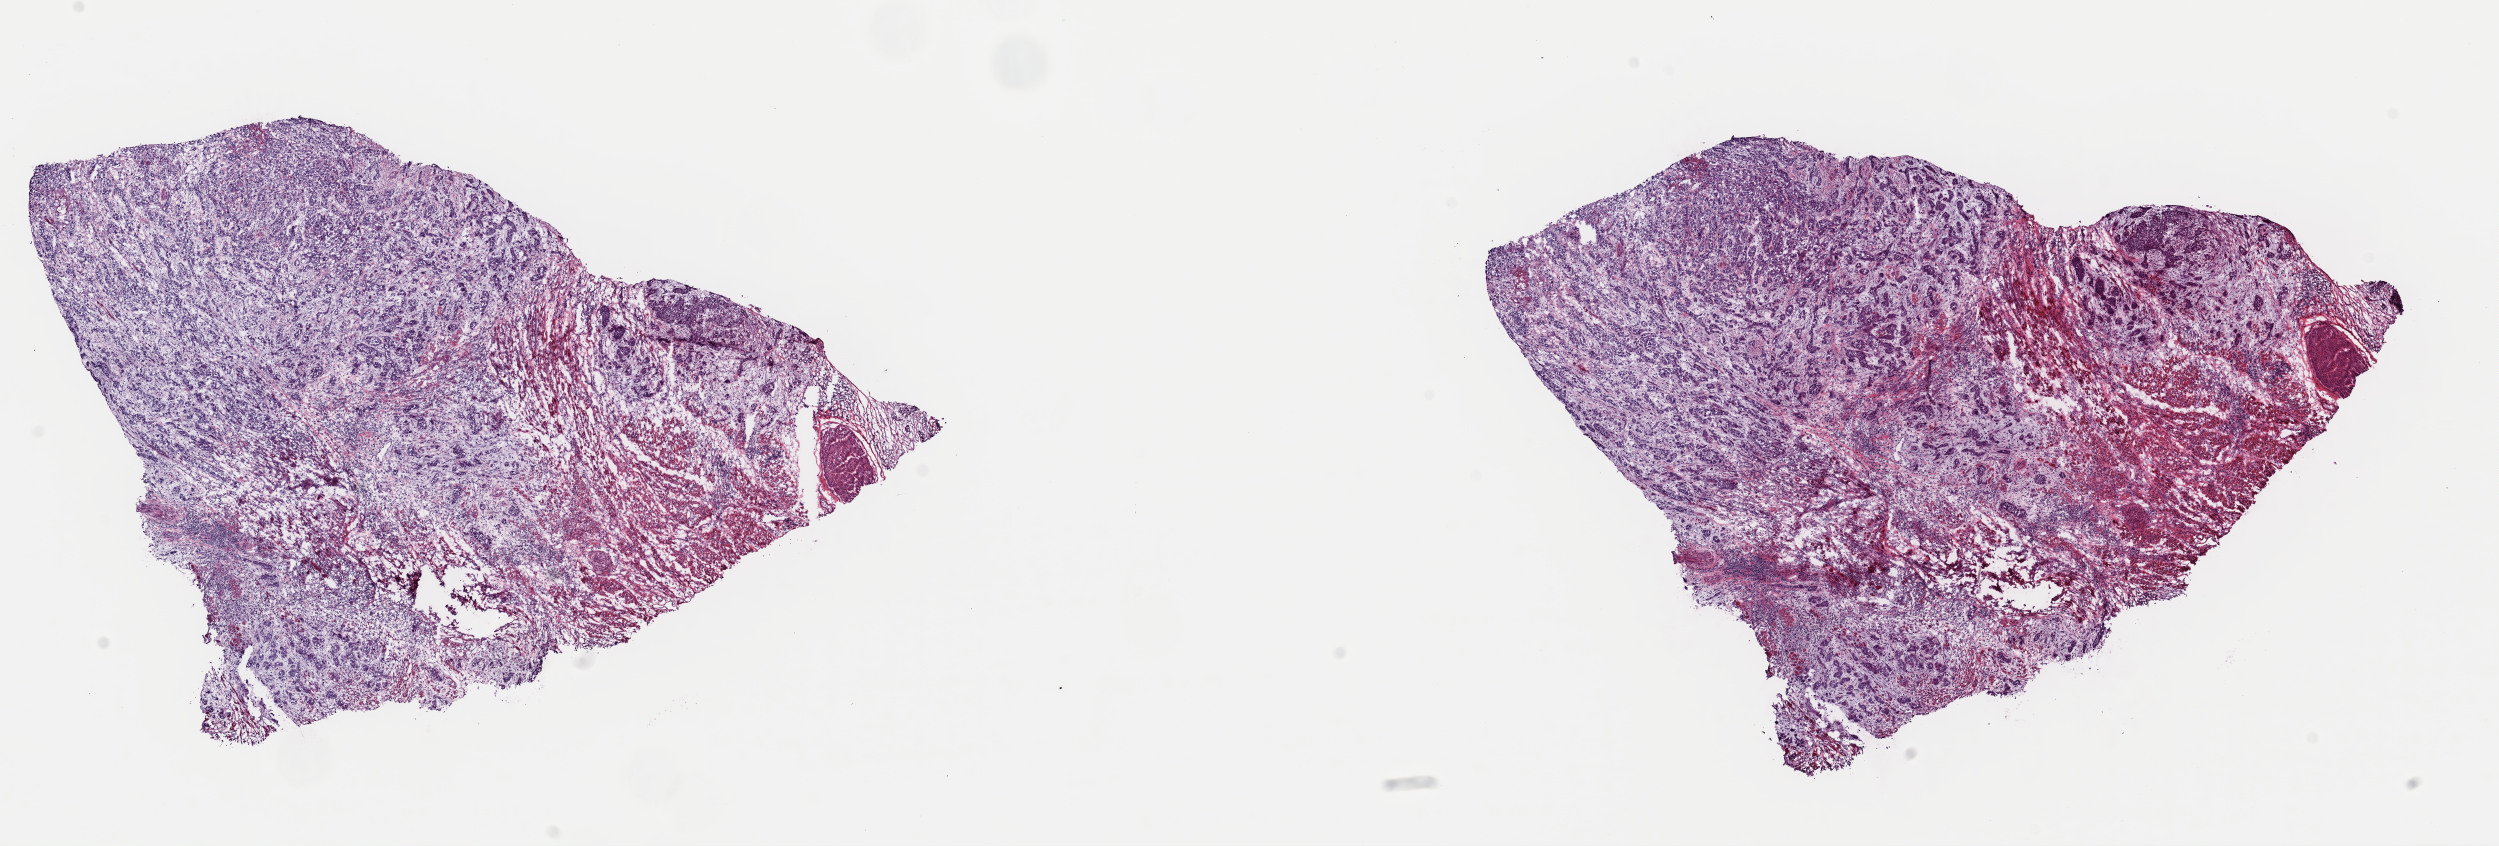
Digitized H&E-stained tissue section (whole slide), shown as a low-resolution overview of the whole scanned area (about 19.7 x 6.7 mm, slide scanned at 40x), frozen section from the top of the tissue portion, head and neck, primary tumour sample. Male patient; age at initial diagnosis 54 years. Histologic grade: G3 (poorly differentiated). Pathologist review of this section (percent, as recorded): tumour cells 50%, tumour nuclei 65%, normal cells 15%, stromal cells 35%, necrosis 0%. Infiltration values recorded for this section: lymphocyte infiltration 8%, monocyte infiltration 2%, neutrophil infiltration 1%.
- TNM: T4a N2 MX
- AJCC pathologic stage: IVA (7th edition)
- histologic diagnosis: Squamous cell carcinoma, NOS (floor of mouth, NOS)